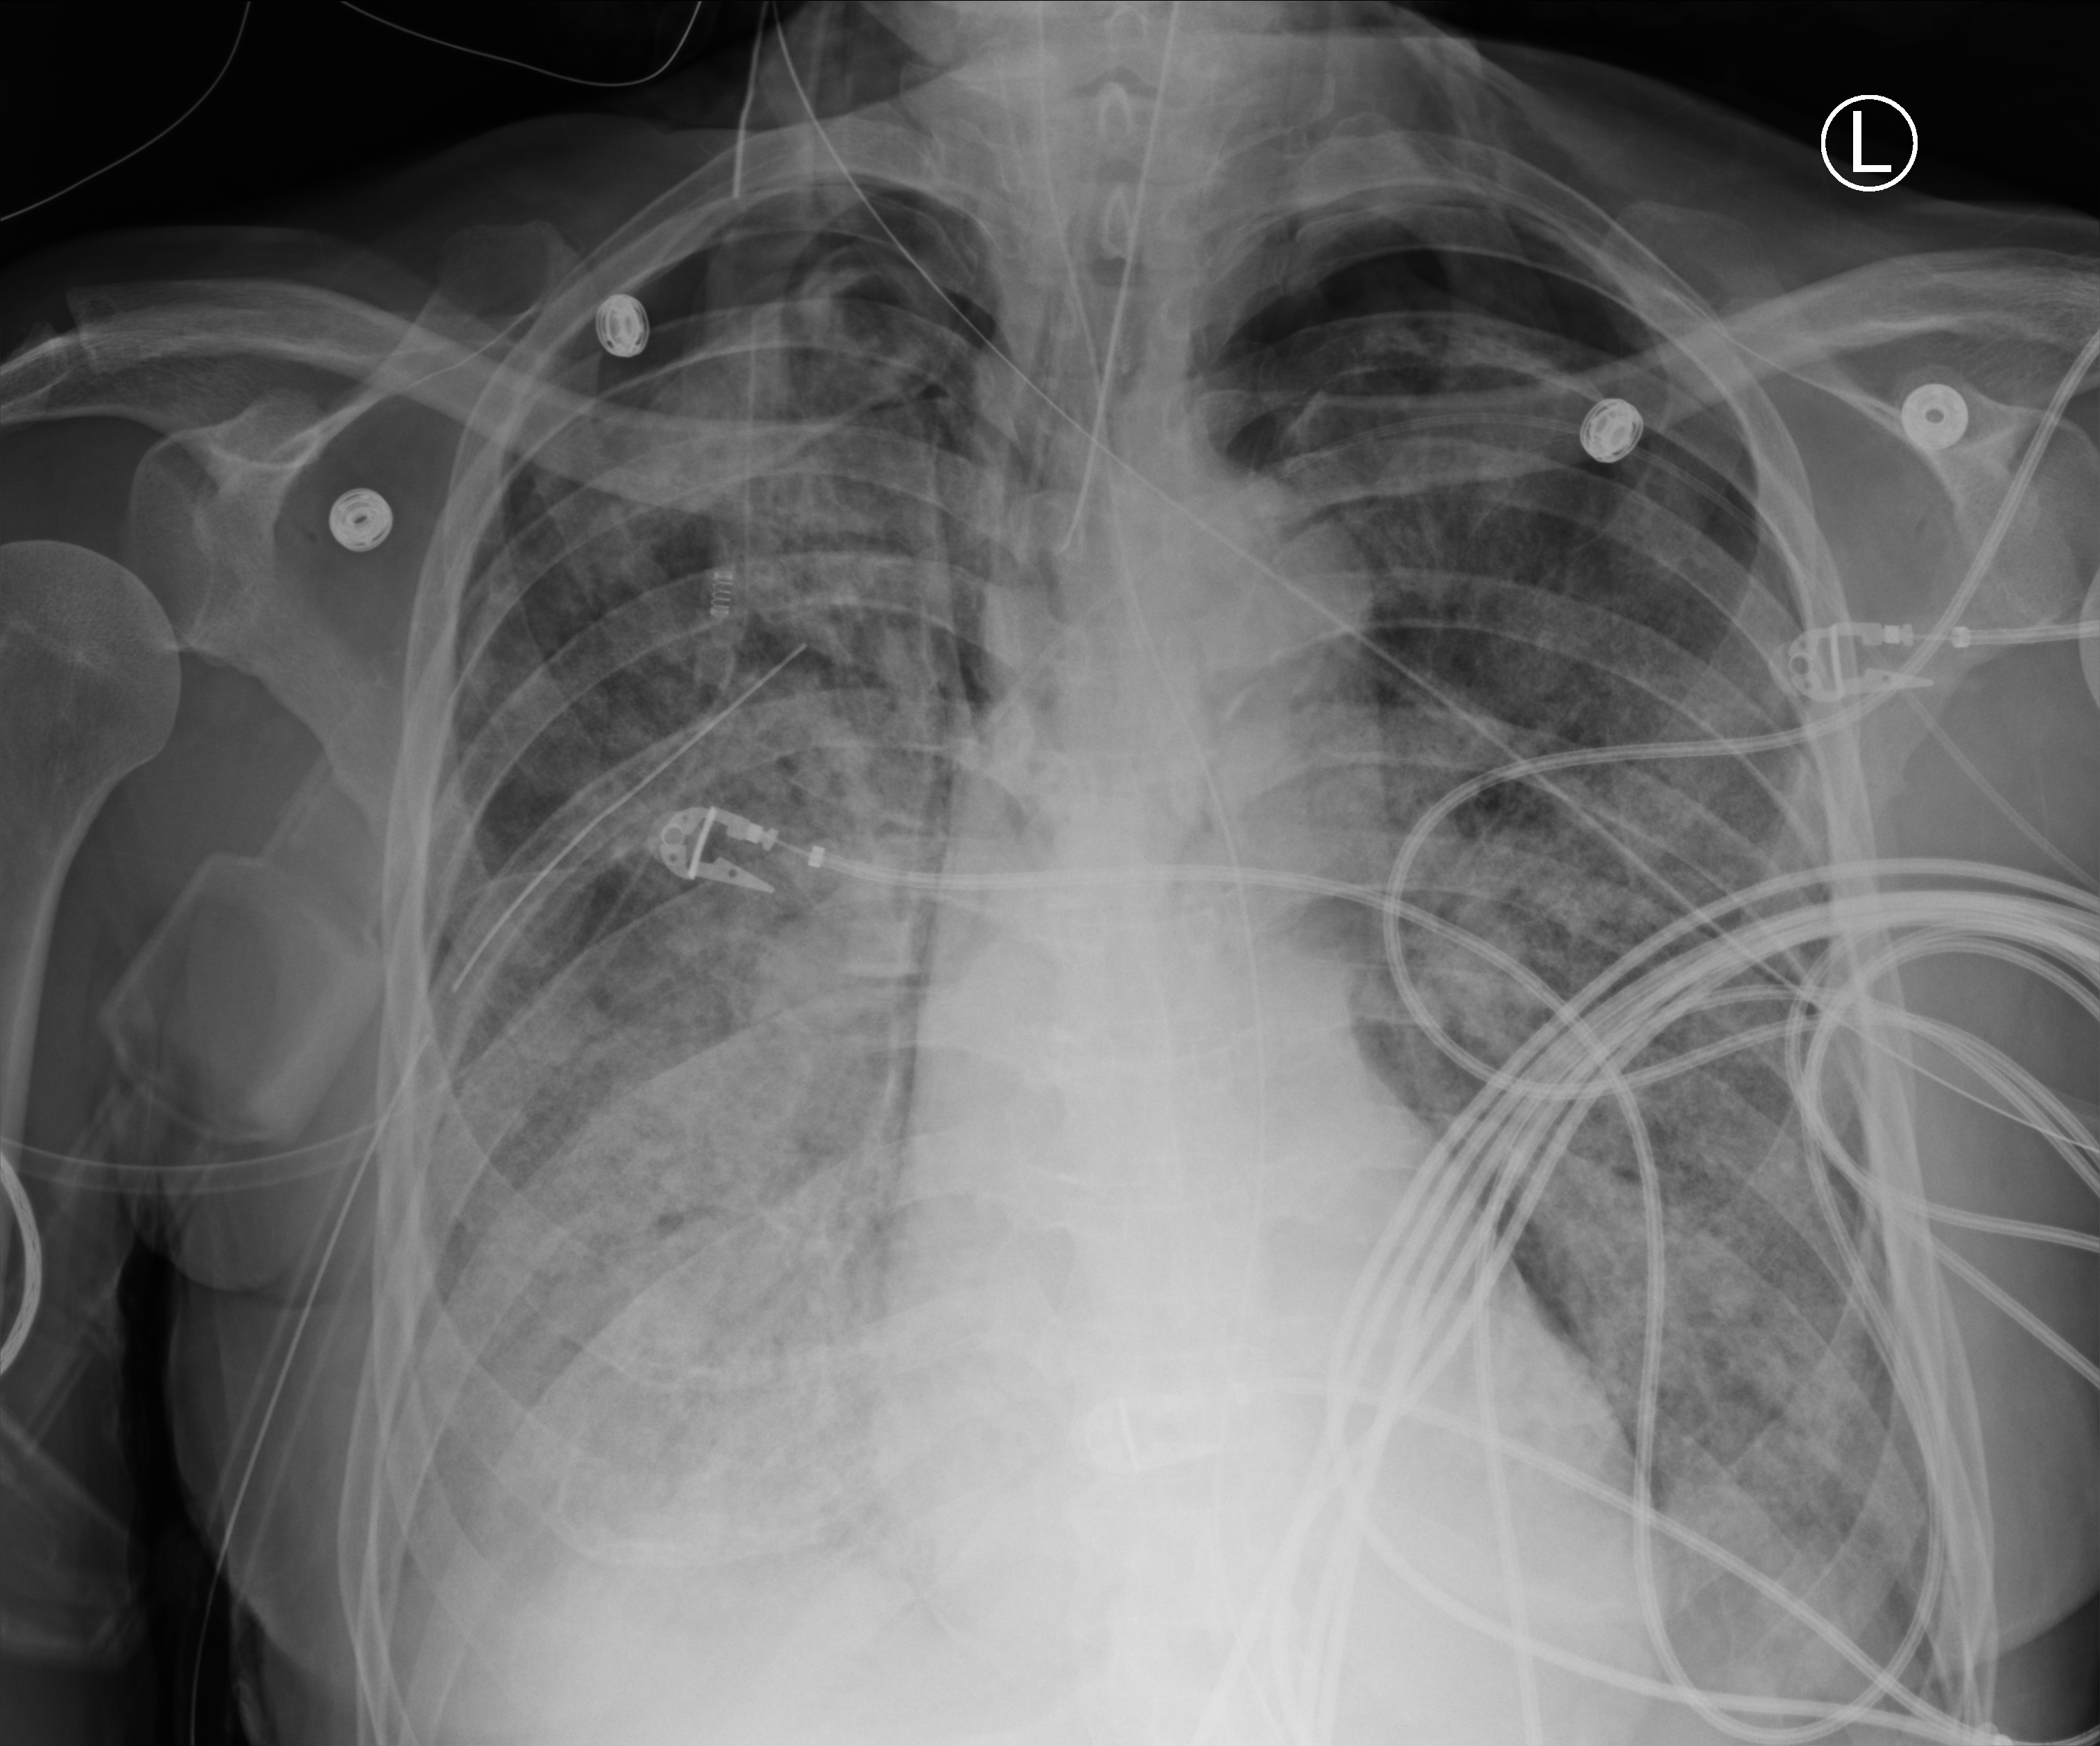
Bedside chest radiograph (computed radiography), anteroposterior (AP) projection. Male patient hospitalised with COVID-19, age 60–74 years.
Admission-level facts for this patient (not findings on this image; timing relative to this image not recorded): length of hospital stay: 31 days; COPD (admission record): no.